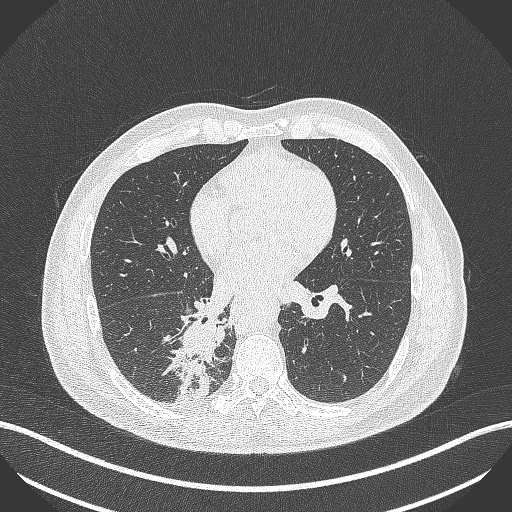
Chest CT, one axial slice; slice 217 of 451 in the series (ordered by position); reconstruction kernel B70f; lung window (W 1500 / L -600 HU); 1 mm slice thickness; 512 × 512 image matrix, field of view 400 × 400 mm. Male patient, age 61 years. From the clinical record (not read from this slice): clinical TNM (as recorded): T1 N0 M0; histopathological grade: G3.
Outlined on this slice (rectangle marked by the reading radiologist):
- lung tumour (recorded histology: small cell carcinoma): box from (x=171, y=315) to (x=222, y=399) px